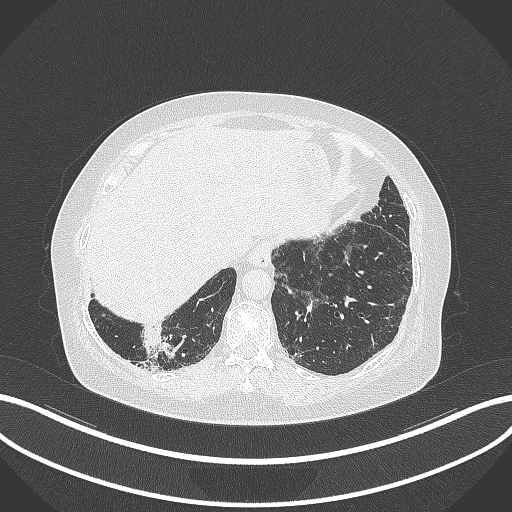
Chest CT, one axial slice. Slice 21 of 296 in the series (ordered by position). Reconstruction kernel B70f. 120 kVp. Lung window (W 1500 / L -600 HU). 1 mm slice thickness. 512 × 512 image matrix. Female patient, age 65 years. Case-level facts recorded for this patient, not image findings: clinical TNM (as recorded): T2b N1 M0.
Outlined on this slice (rectangle marked by the reading radiologist):
- lung tumour (recorded histology: adenocarcinoma): bounding box [x1, y1, x2, y2] px = [138, 325, 183, 361]